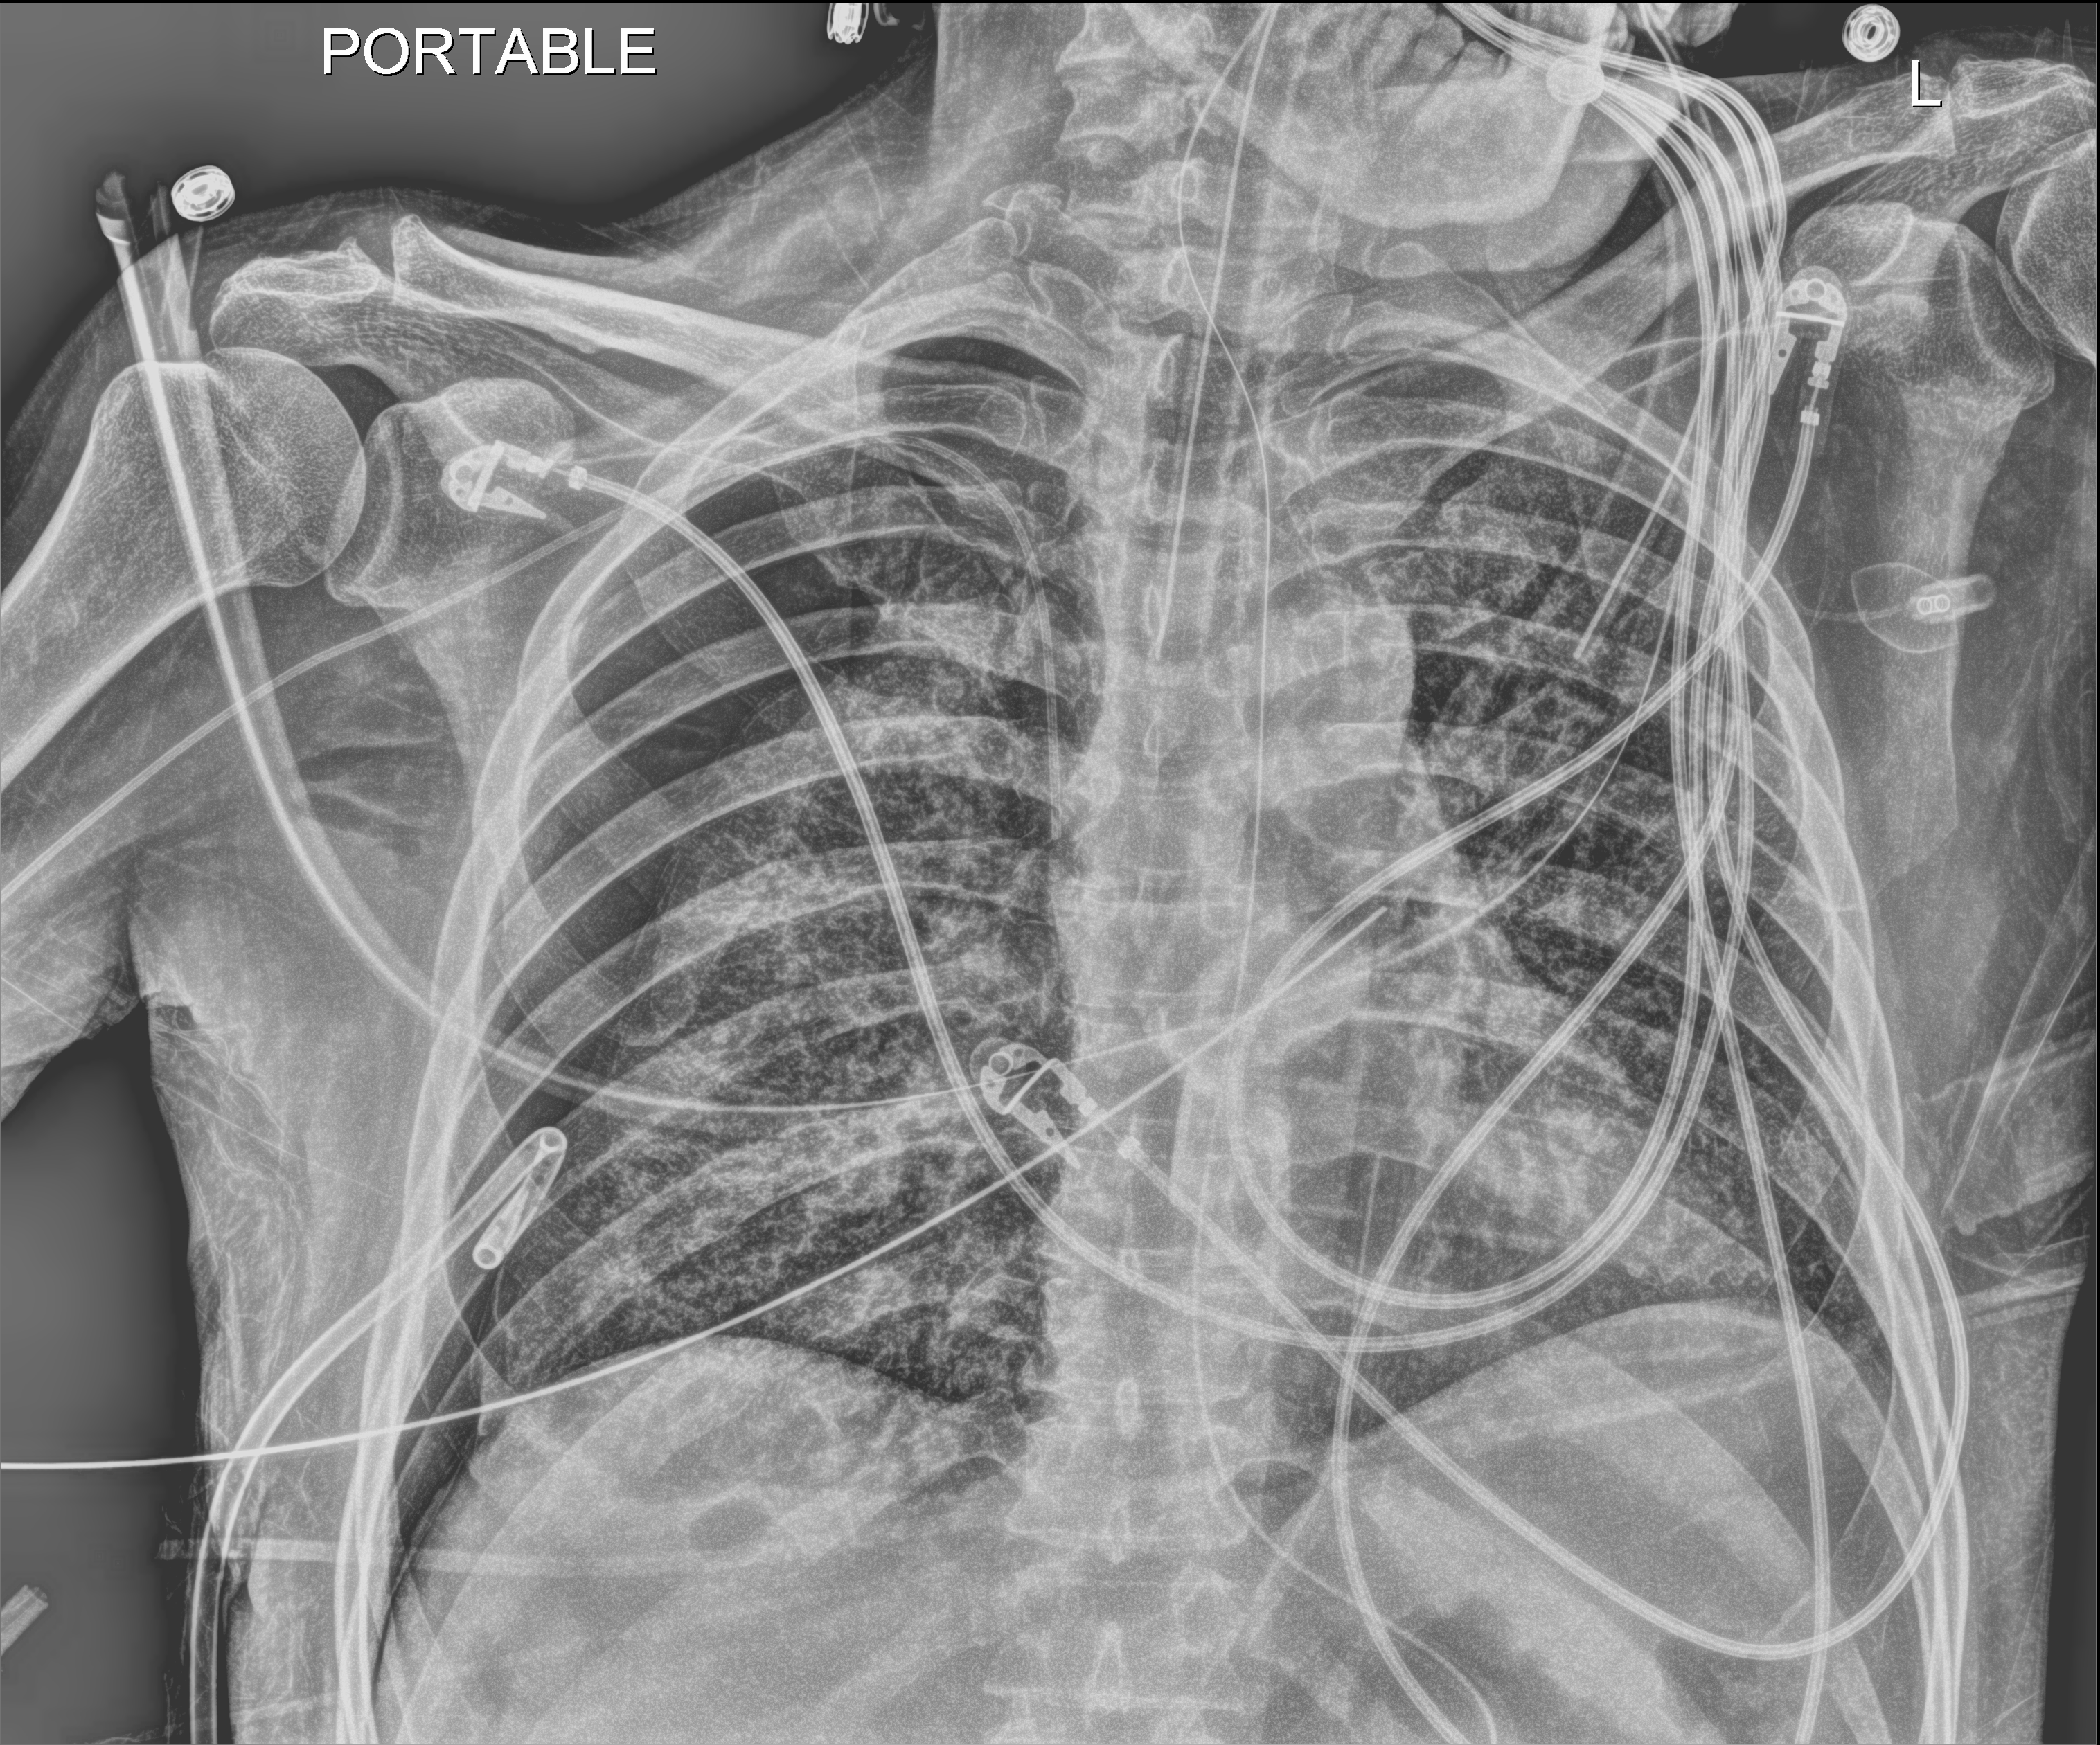
Chest X-ray (portable); anteroposterior (AP) projection. Male patient hospitalised with COVID-19, age 18–59 years.
Admission-level facts for this patient (not findings on this image; timing relative to this image not recorded): smoking status (admission record): never.